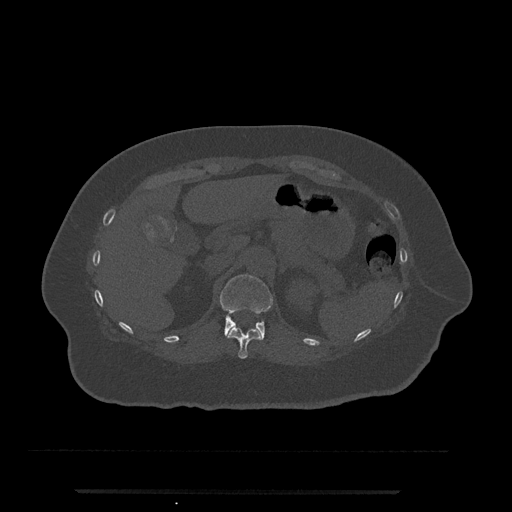
CT including the spine, one axial slice; slice 197 of 797 in the series (ordered by position); reconstruction kernel Br40s/3; bone window (W 1800 / L 400 HU); 0.5 mm slice thickness; 512 × 512 image matrix, field of view 440 × 440 mm. Female patient, age 51 years. From the clinical record (not read from this slice): primary cancer: neuro; vertebrae with lytic lesions (as recorded): T8.
Annotated regions visible in this slice (semi-automatically segmented with operator editing):
- T11 vertebra: box from (x=226, y=327) to (x=261, y=359) px
- T12 vertebra: (x=220, y=274)–(x=273, y=341)